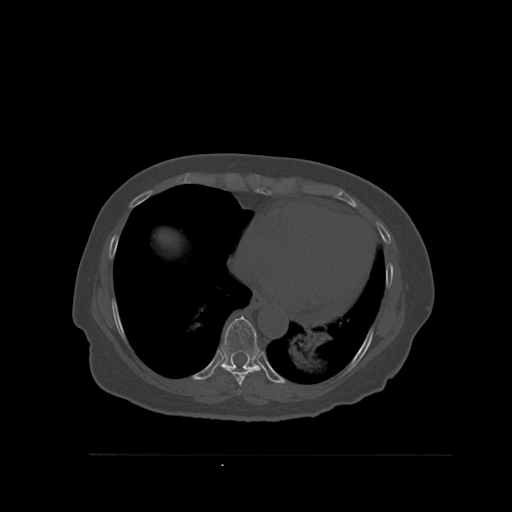
CT including the spine, one axial slice. Position 341 of 527 along the scan axis. Bone window (W 1800 / L 400 HU). 1.5 mm slice thickness. 512 × 512 image matrix, field of view 470 × 470 mm. Patient: female, 73 years. Case-level facts recorded for this patient, not image findings: primary cancer: breast; vertebrae with lytic lesions (as recorded): L2.
Outlined on this slice (semi-automatically segmented with operator editing):
- T7 vertebra: box from (x=239, y=391) to (x=241, y=393) px
- T8 vertebra: (x=226, y=367)–(x=261, y=386)
- T9 vertebra: (x=217, y=315)–(x=268, y=378)